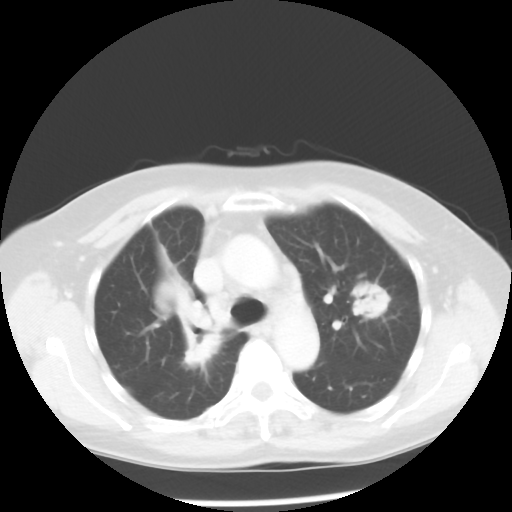
Chest CT, one axial slice. Slice 35 of 52 in the series (ordered by position). 100 kVp. Lung window (W 1500 / L -600 HU). 5 mm slice thickness. 512 × 512 image matrix. Patient: female, 60 years. From the clinical record (not read from this slice): clinical TNM (as recorded): T2 N1 M1a.
Annotated regions visible in this slice (bounding box drawn by a radiologist):
- lung tumour (recorded histology: adenocarcinoma): bounding box (x1, y1, x2, y2) in pixels: (157, 277, 227, 378)